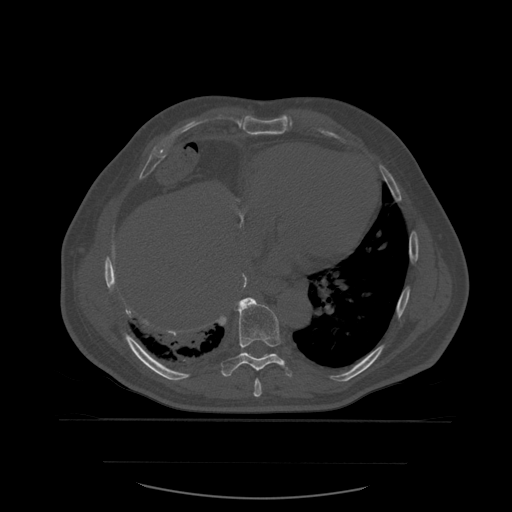
CT including the spine, one axial slice; bone window (W 1800 / L 400 HU); 1.25 mm slice thickness; 512 × 512 image matrix, field of view 479 × 479 mm. Patient age 71 years. From the clinical record (not read from this slice): primary cancer: lung; vertebrae with lytic lesions (as recorded): T1, T2, L5, S1.
Outlined on this slice (semi-automatic segmentation, software-assisted and operator-edited):
- T8 vertebra: box from (x=254, y=379) to (x=262, y=397) px
- T9 vertebra: (x=220, y=298)–(x=293, y=377)